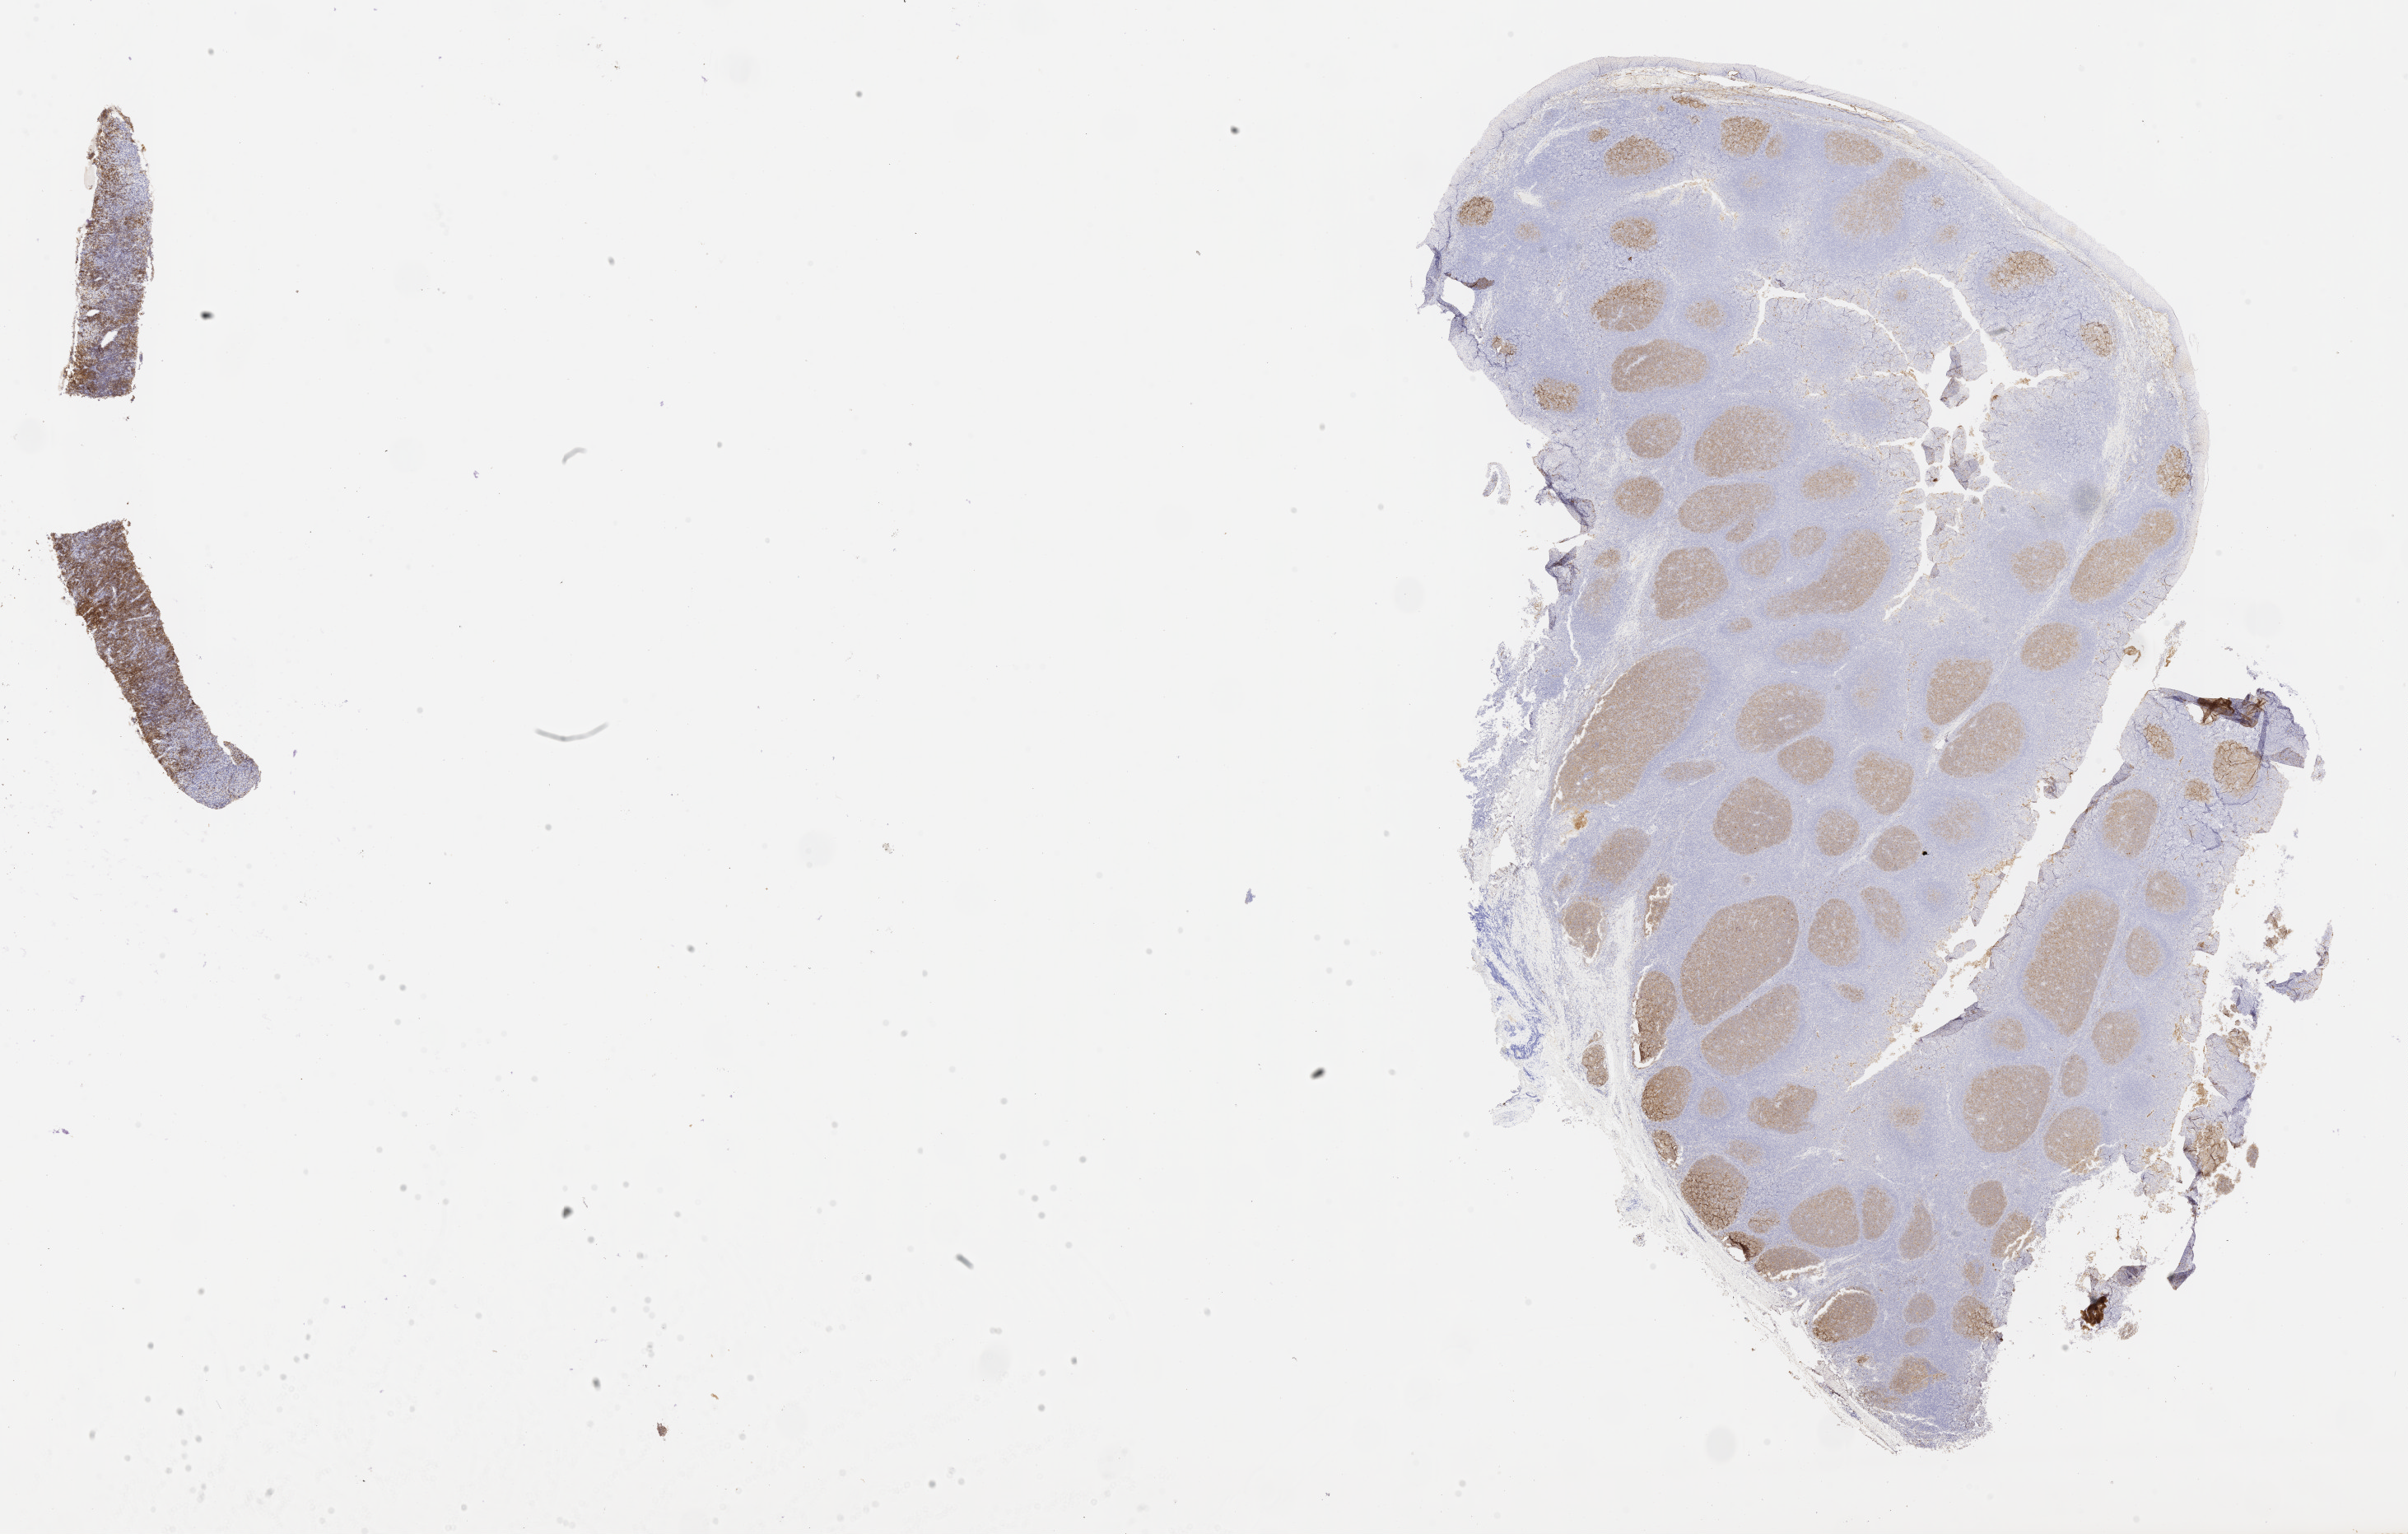
IHC for CD10, whole-slide image — whole scanned area (about 23.6 x 15.1 mm) shown as a low-resolution overview. Patient sex: male.
Specimen: tumor tissue.